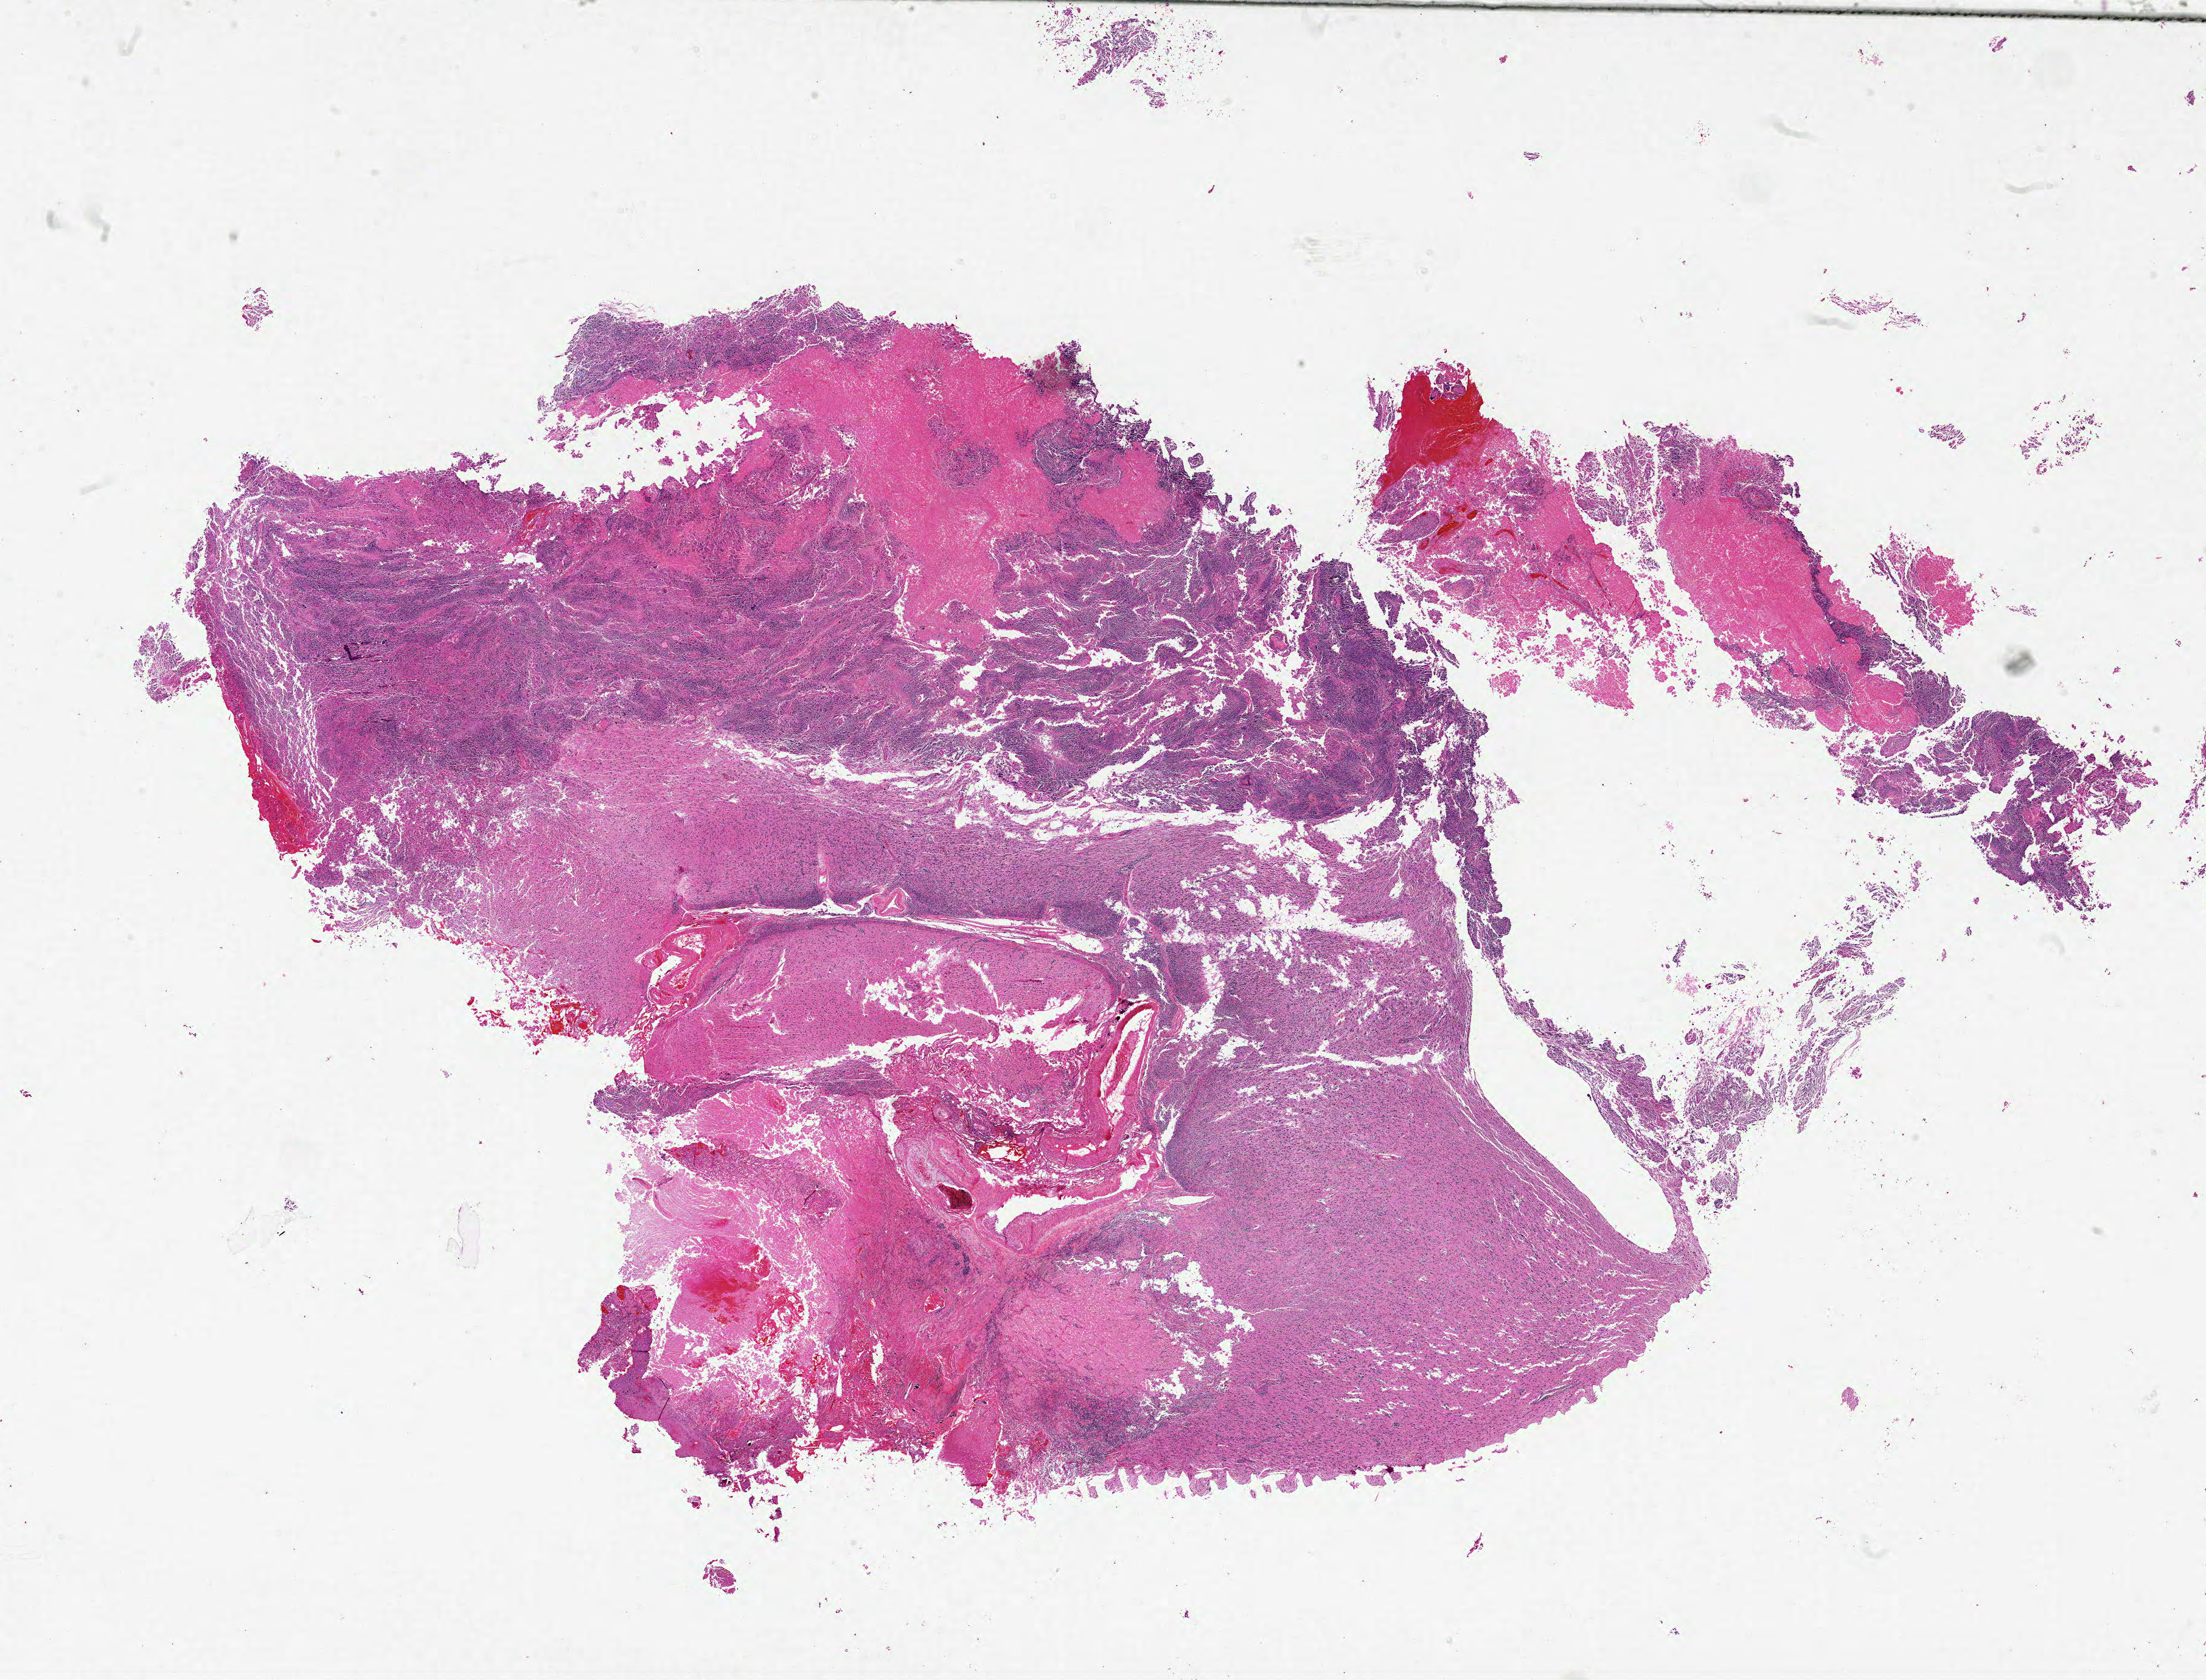
Whole-slide histology image, Hematoxylin and eosin (H&E) stained — whole scanned area (about 29.0 x 22.1 mm, acquisition: 20x scan) shown as a low-resolution overview. Formalin-fixed paraffin-embedded (FFPE) diagnostic section. Brain, primary tumour sample. Male patient; age at initial diagnosis 24 years.
Histologic diagnosis: Glioblastoma.